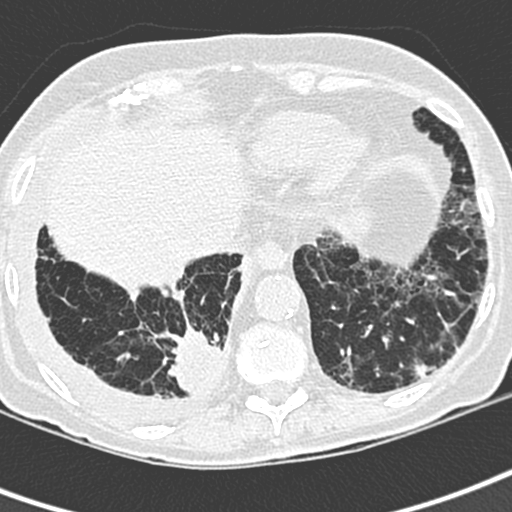
Low-dose screening chest CT, one axial slice. Slice 69 of 220 in the series (ordered by position). Lung window (W 1500 / L -600 HU). 1.3 mm slice thickness. 512 × 512 image matrix, field of view 288 × 288 mm.
Annotated regions visible in this slice (outlined manually by an expert reader):
- lesion 1 (tumor, lower lobe of right lung): bounding box [x1, y1, x2, y2] px = [168, 326, 223, 395]
- lesion 2 (nodule, lower lobe of left lung): [415, 365, 429, 377]